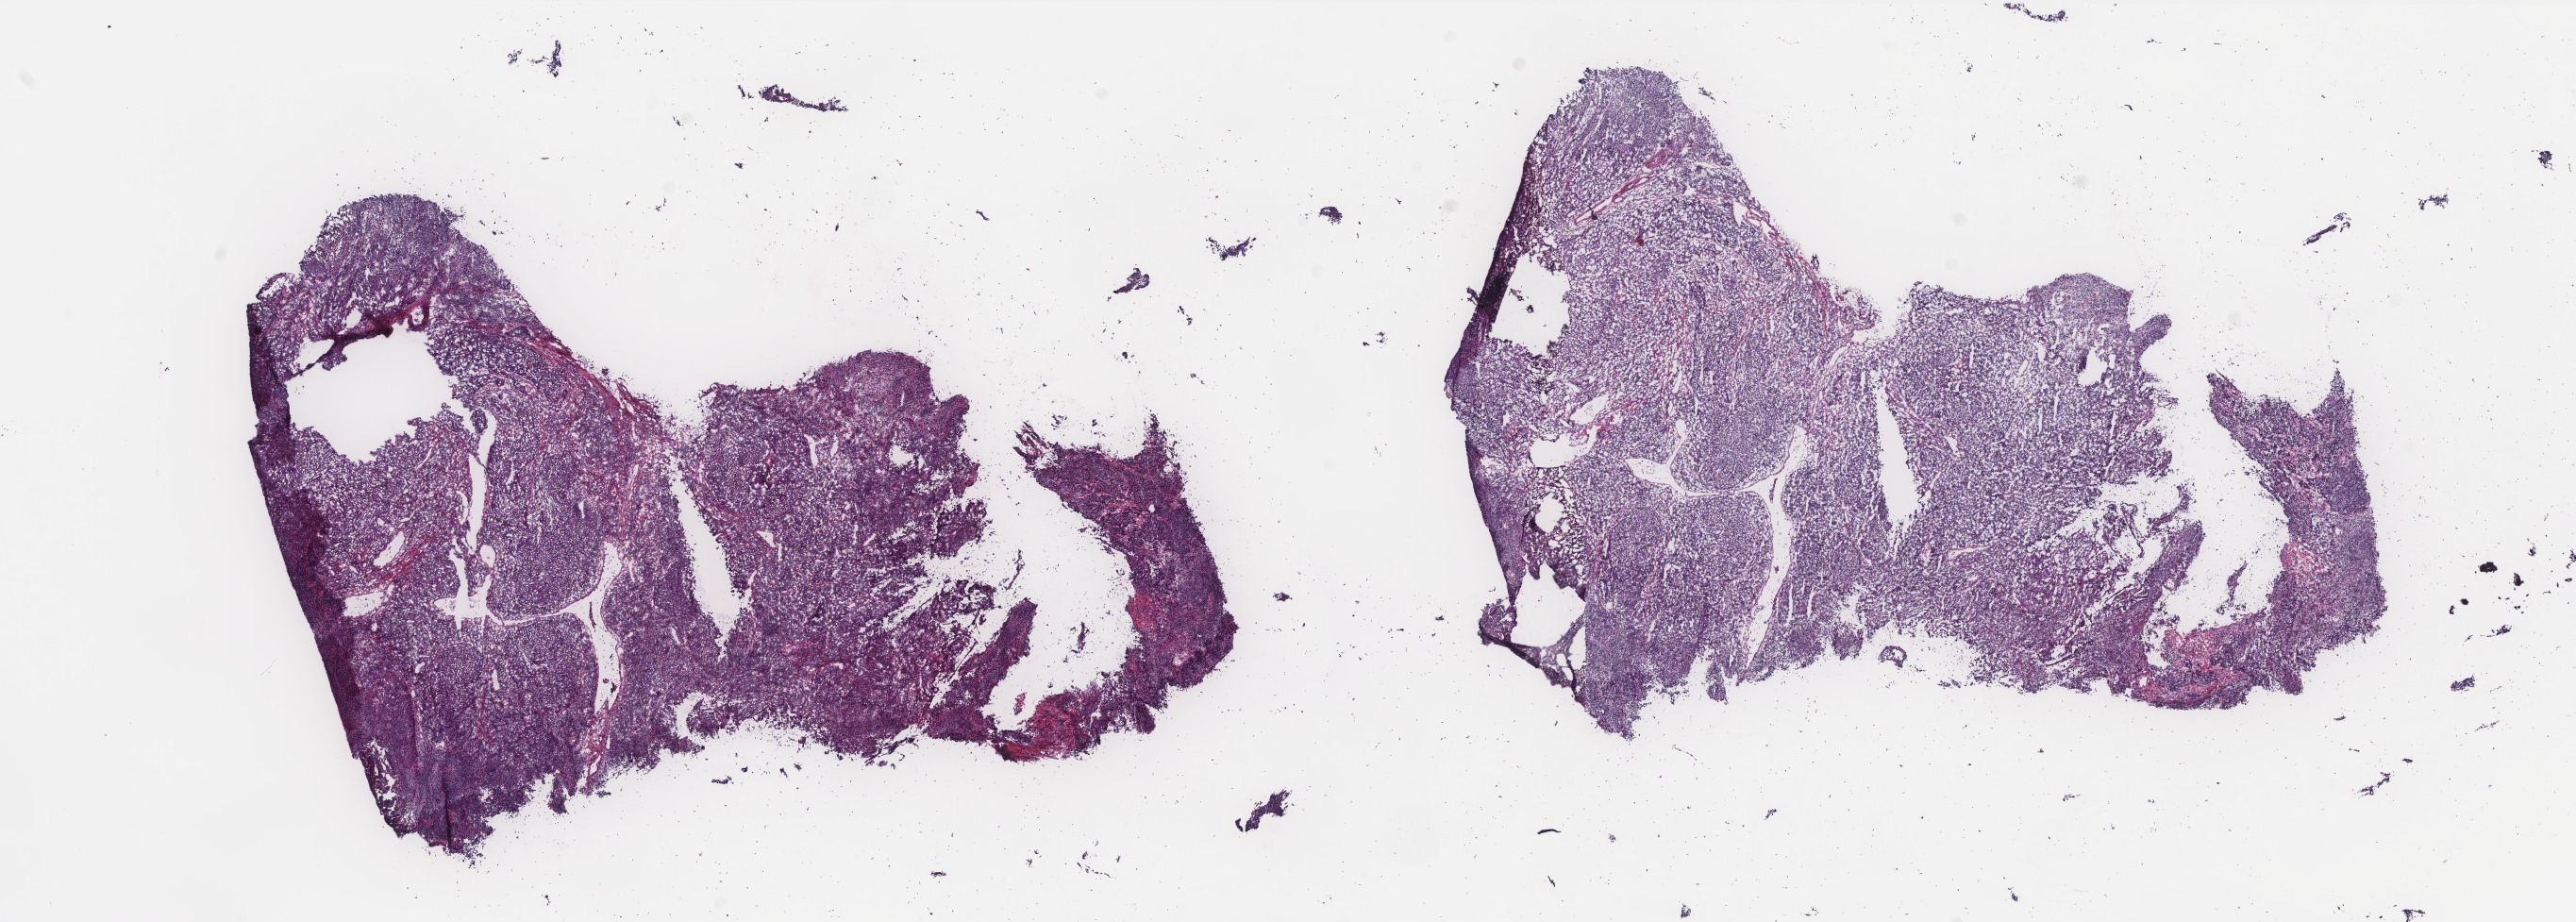
H&E-stained whole-slide image, shown as a low-resolution overview of the whole scanned area (about 21.9 x 7.8 mm), frozen section from the top of the tissue portion, cervix, primary tumour sample. Female, age 53 years at initial diagnosis. Histologic grade: G2 (moderately differentiated). Pathologist review of this section (percent, as recorded): tumour cells 90%, tumour nuclei 90%, normal cells 0%, stromal cells 10%, necrosis 0%. Infiltration values recorded for this section: lymphocyte infiltration 60%, monocyte infiltration 2%, neutrophil infiltration 3%.
Lymph nodes positive (case pathology): 0 of 59 examined. Diagnosis: Squamous cell carcinoma, NOS (cervix uteri). FIGO stage: IB.